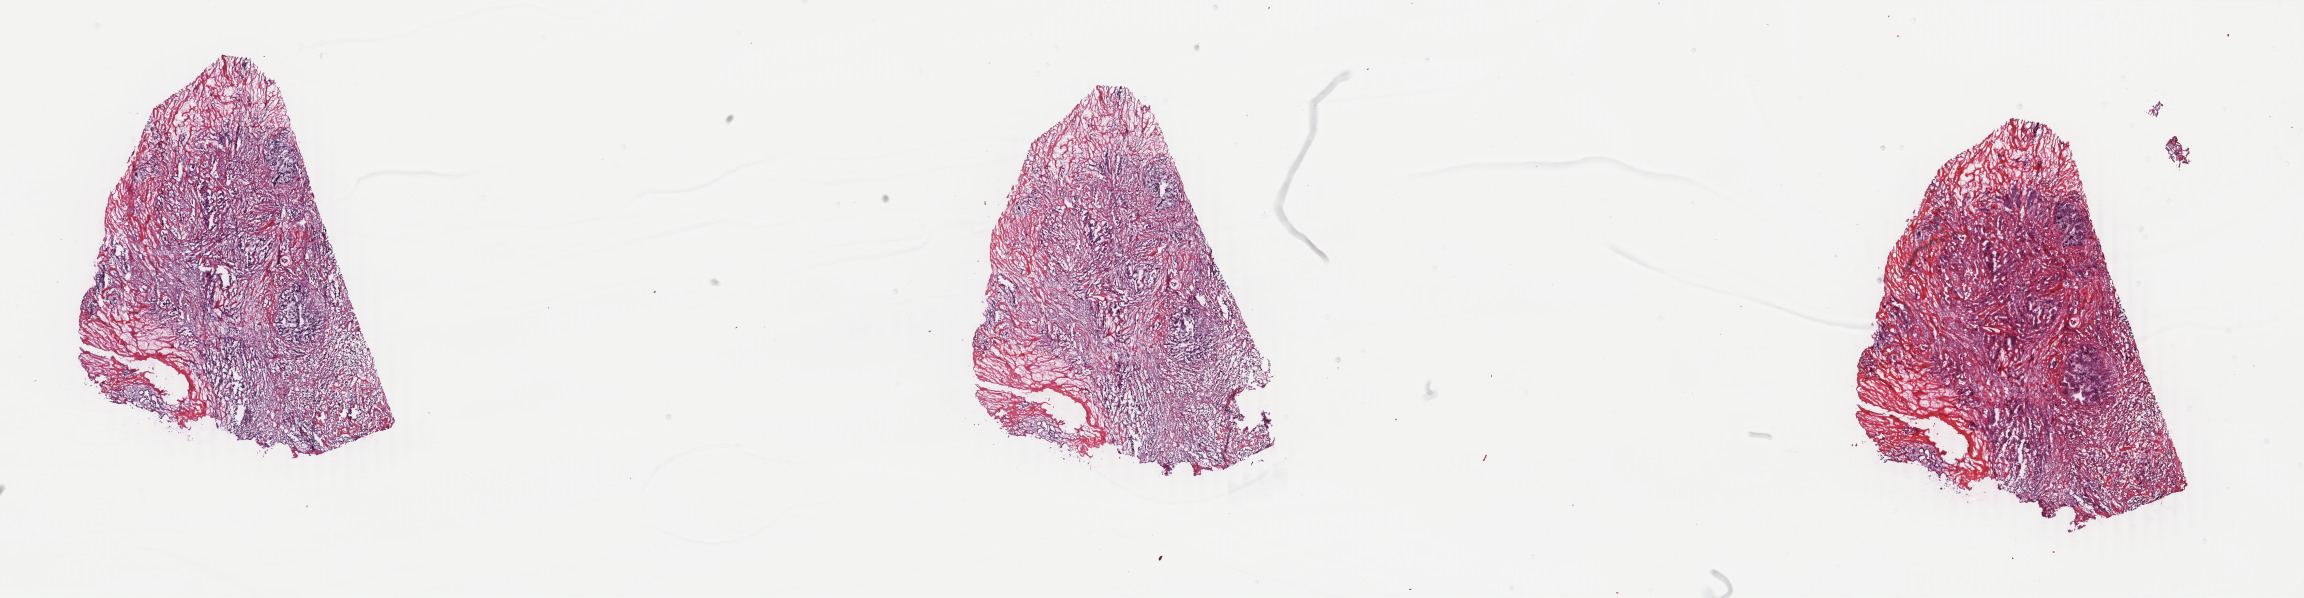
Hematoxylin and eosin (H&E) stained whole-slide image — whole scanned area (about 36.6 x 9.5 mm) shown as a low-resolution overview; frozen section from the top of the tissue portion; primary tumour sample from the breast. Female patient; age at initial diagnosis 63 years. Slide review estimates, as recorded: tumour cells 75%, tumour nuclei 75%.
Pathologic diagnosis: Infiltrating duct carcinoma, NOS.